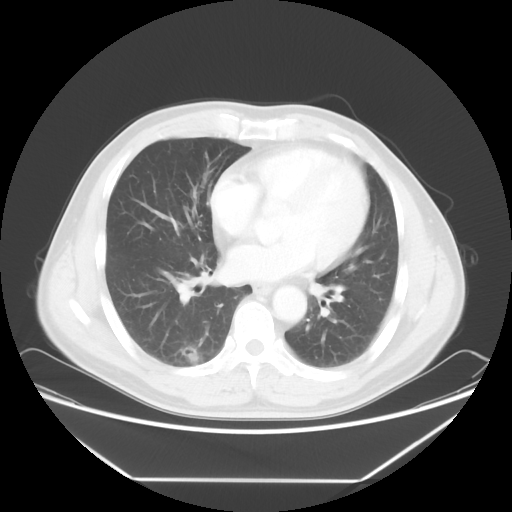
Chest CT, one axial slice. Position 31 of 65 along the scan axis. 120 kVp. Lung window (W 1500 / L -600 HU). 5 mm slice thickness. 512 × 512 image matrix, field of view 418 × 418 mm. Male patient, age 50 years. Case-level facts recorded for this patient, not image findings: clinical TNM (as recorded): T1c N0 M0; histopathological grade: G3.
Structures marked on this image (rectangle marked by the reading radiologist):
- lung tumour (recorded histology: adenocarcinoma): bounding box [x1, y1, x2, y2] px = [175, 343, 204, 368]